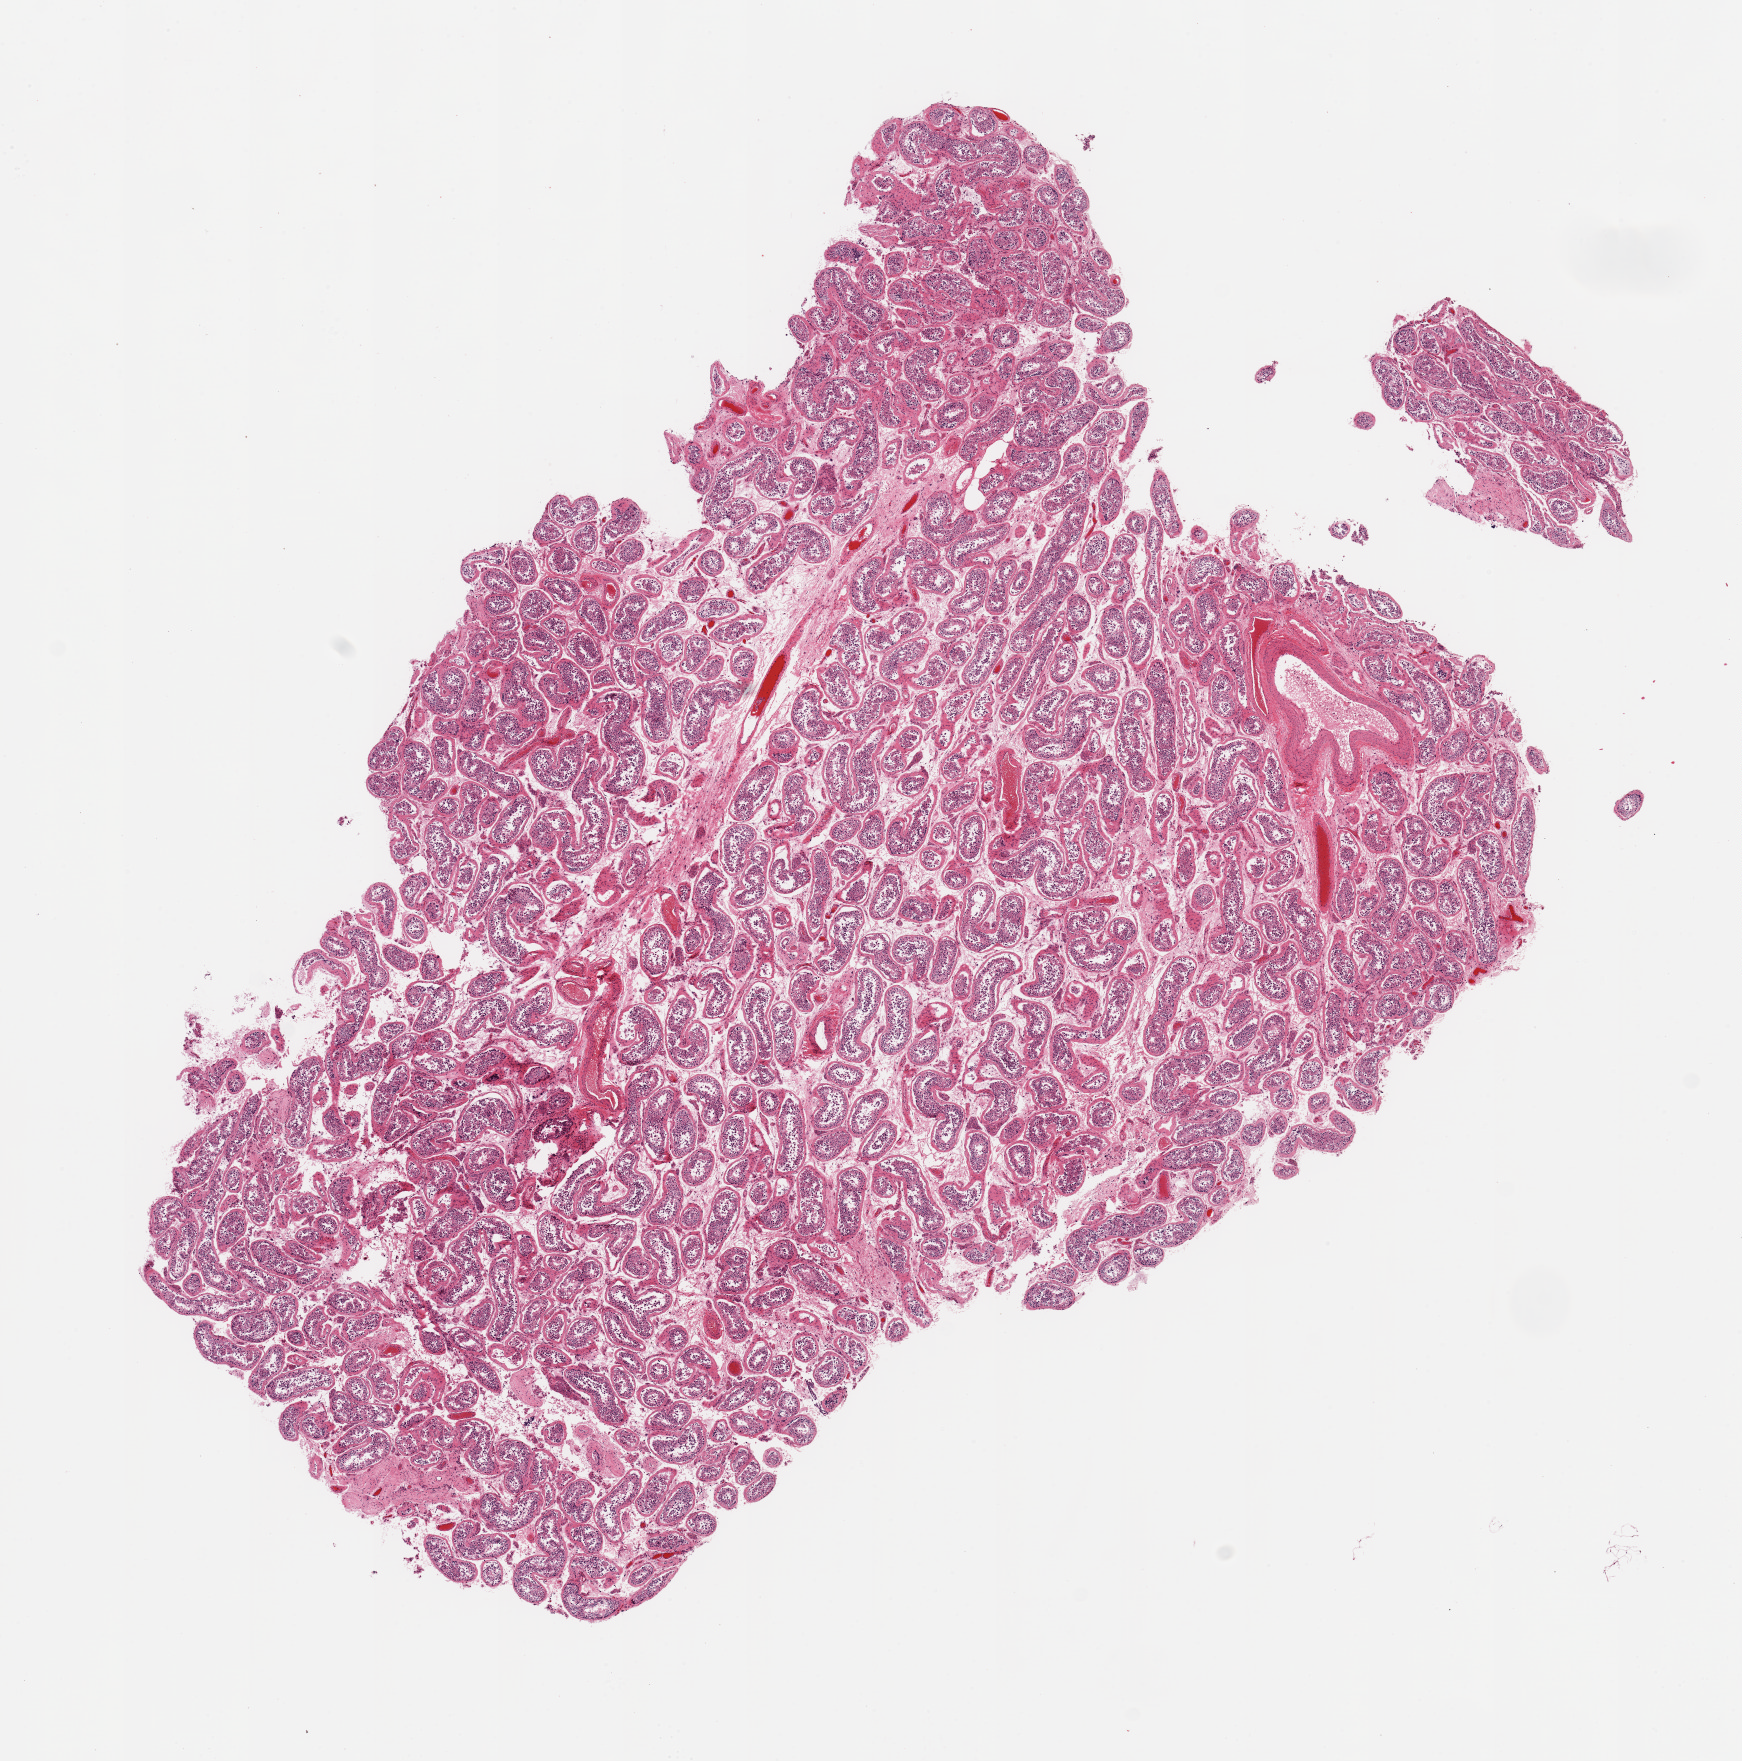
Haematoxylin and eosin whole-slide image, brightfield — a low-resolution overview of the entire scanned area, about 13.8 x 13.9 mm, PAXgene-fixed, paraffin-embedded tissue, section of testis (target tissue), donor tissue sample. Male donor.
Reviewer comment on this tissue sample: 1 piece, moderate/severe autolysis. spermatogenesis appears present but reduced.